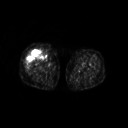
FDG PET of an extremity soft-tissue mass (from a PET/CT study), one axial slice. Position 228 of 311 along the scan axis. 128 × 128 image matrix, field of view 500 × 500 mm. Female patient, age 57 years. From the clinical record (not read from this slice): histological type: pleiomorphic undifferentiated sarcoma; grade: high; site of the primary tumour: right quadricep.
Structures marked on this image (expert contour drawn on MRI and transferred to this co-registered scan by the dataset authors):
- tumour plus oedema (research contour): bounding box <26,50,44,69> (left, top, right, bottom; pixels)